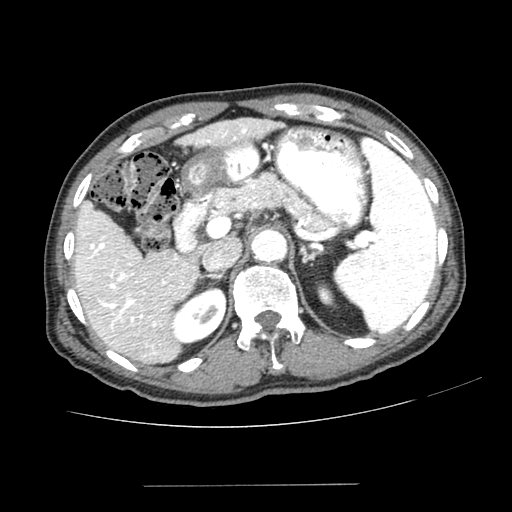
Contrast-enhanced abdominal CT (liver protocol), one axial slice. Position 151 of 187 along the scan axis. Reconstruction kernel SOFT. One of 2 acquisitions stored at this slice position. Soft-tissue window (W 400 / L 40 HU). 2.5 mm slice thickness. 512 × 512 image matrix. Case-level facts recorded for this patient, not image findings: diagnosis: hepatocellular carcinoma (patient treated with transarterial chemoembolisation; whether this scan precedes or follows treatment is not stated here); TNM stage (as recorded): Stage-I; Child-Pugh class: A; tumour differentiation: poorly differentiated; tumour size: 1.6 cm.
Annotated regions visible in this slice (semi-automatic segmentation, software-assisted and operator-edited):
- liver parenchyma outside the tumour (the mass and vessels are separate outlines, so this box may not span the whole liver): box from (x=74, y=118) to (x=274, y=362) px
- liver vessels: (x=87, y=127)–(x=247, y=355)